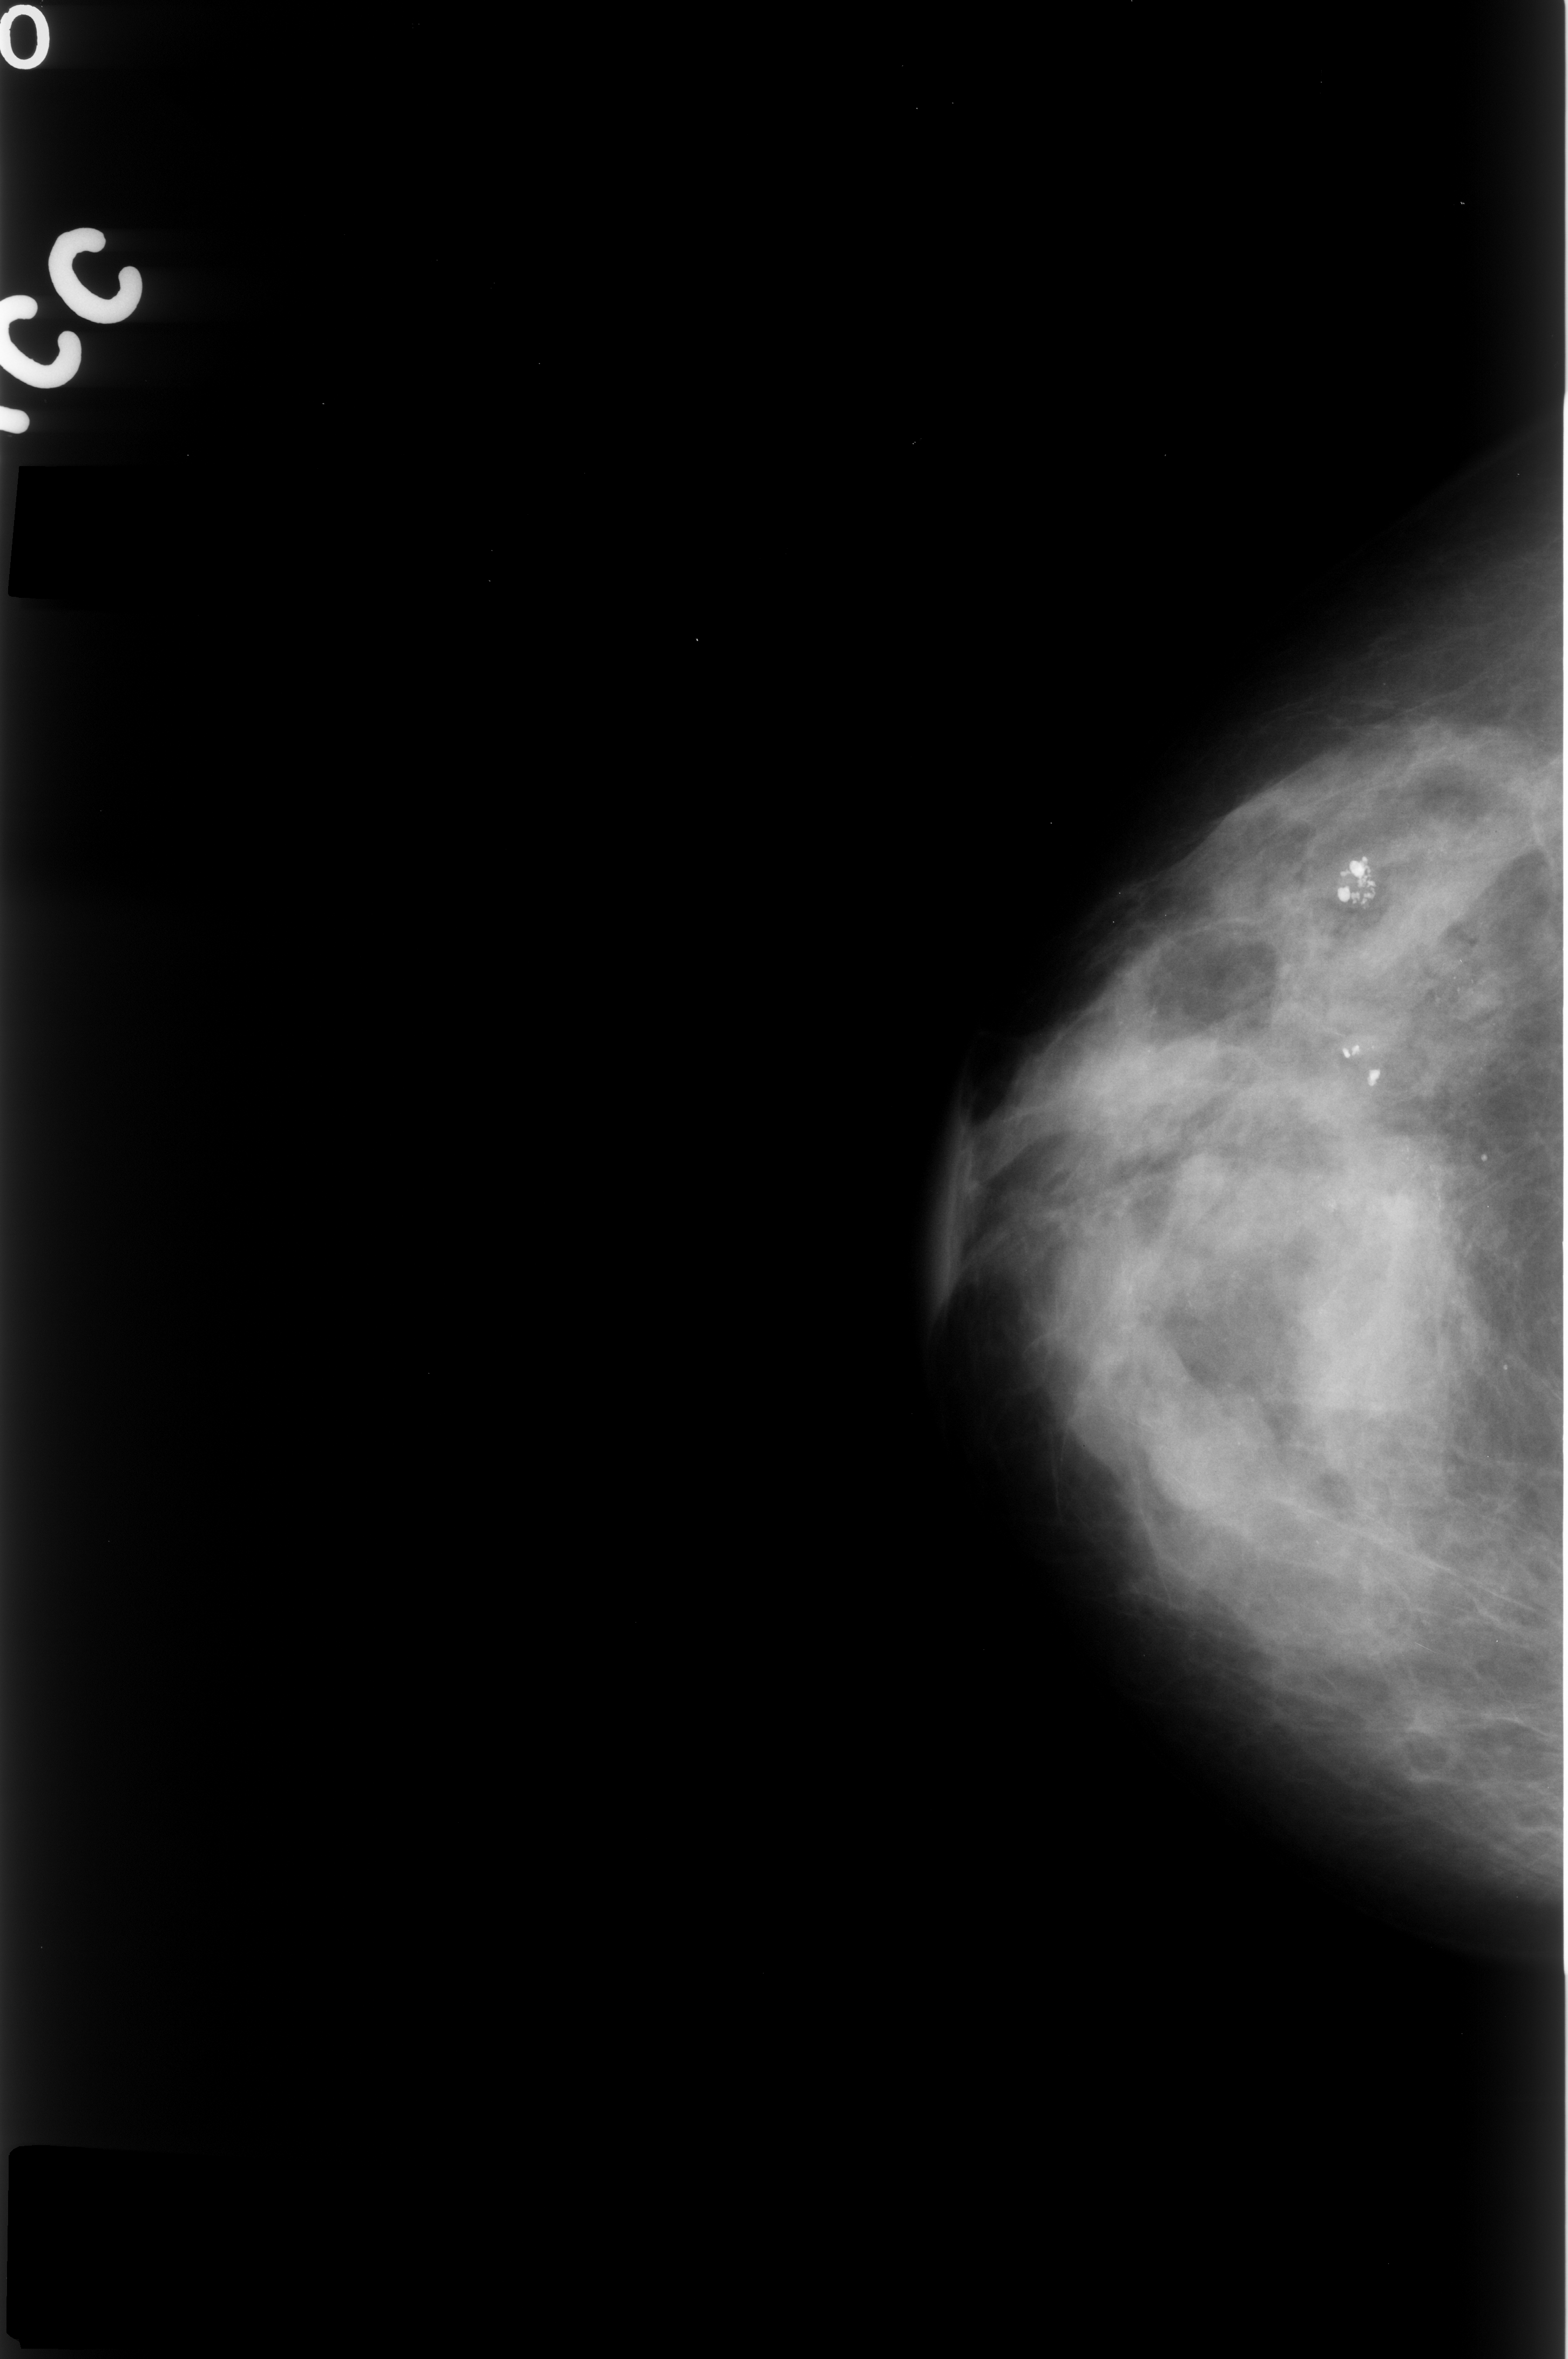
Digitized screen-film mammogram, right breast, CC view, BI-RADS breast density category 3 (scale 1–4).
Abnormality record for this image: calcifications, morphology amorphous, distribution clustered; BI-RADS assessment category 4; pathology (as recorded): benign.